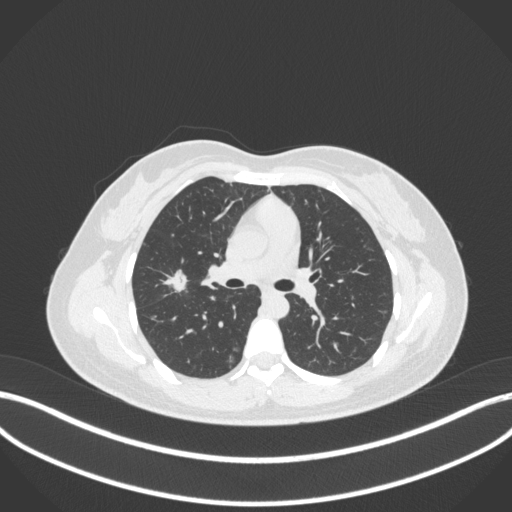
Chest CT, one axial slice; position 199 of 214 along the scan axis; reconstruction kernel B31f; 120 kVp; lung window (W 1500 / L -600 HU); 1 mm slice thickness; 512 × 512 image matrix, field of view 400 × 400 mm. Female patient, age 33 years. From the clinical record (not read from this slice): clinical TNM (as recorded): T1c N0 M0.
Structures marked on this image (bounding box drawn by a radiologist):
- lung tumour (recorded histology: adenocarcinoma): bounding box [x1, y1, x2, y2] px = [162, 268, 194, 298]